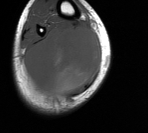
MRI of an extremity soft-tissue mass, one axial slice; slice 41 of 76 in the series (ordered by position); MR volume resampled by the dataset authors to the PET/CT grid (not the native acquisition matrix); 3.27 mm slice thickness; 148 × 133 image matrix. Male patient. From the clinical record (not read from this slice): histological type: liposarcoma - round cell; grade: high; site of the primary tumour: right calf.
Structures marked on this image (expert contour drawn on MRI and transferred to this co-registered scan by the dataset authors):
- gross tumour volume (mass): bounding box (x1, y1, x2, y2) in pixels: (26, 26, 101, 106)